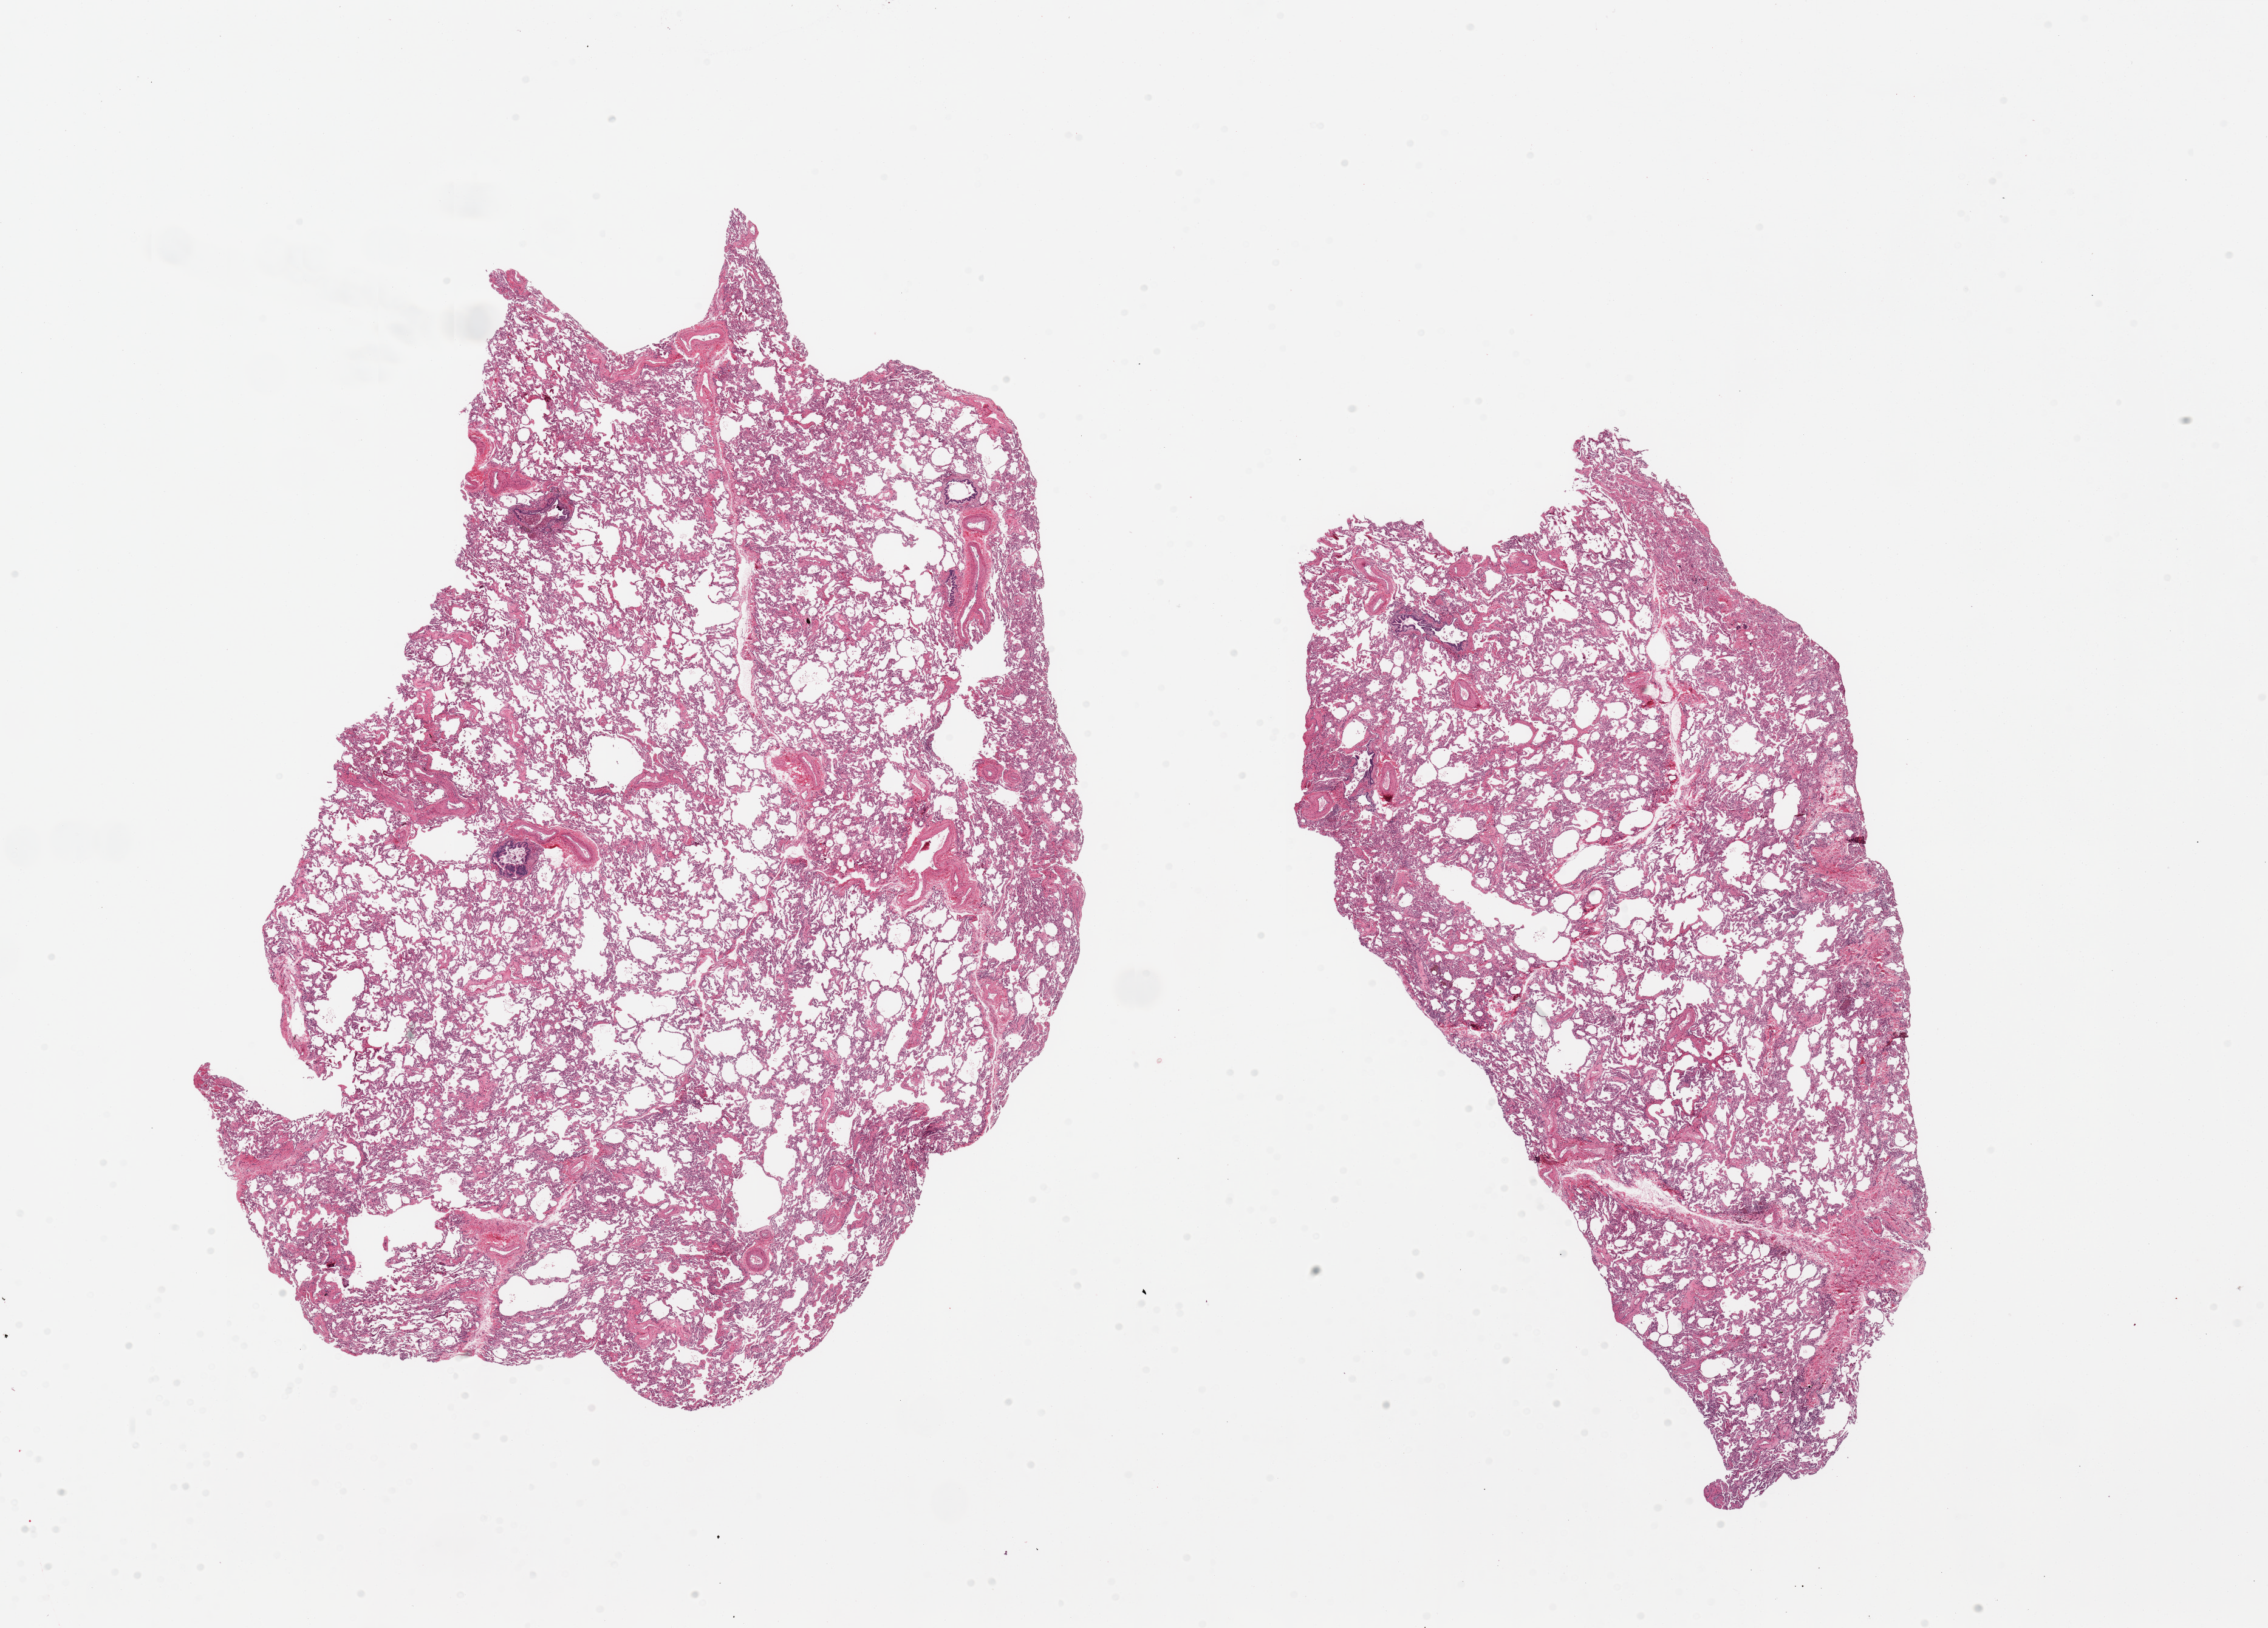
Whole-slide image, haematoxylin and eosin stain, low-resolution overview of the scanned area, about 29.5 x 21.2 mm (from a 20x scan). PAXgene-fixed paraffin-embedded (PFPE) section. Section of lung (target tissue). Tissue donor sample. Donor: male.
* pathologist's review note for this sample: 2 pieces; thick walled vessels, emphysematous-like changes